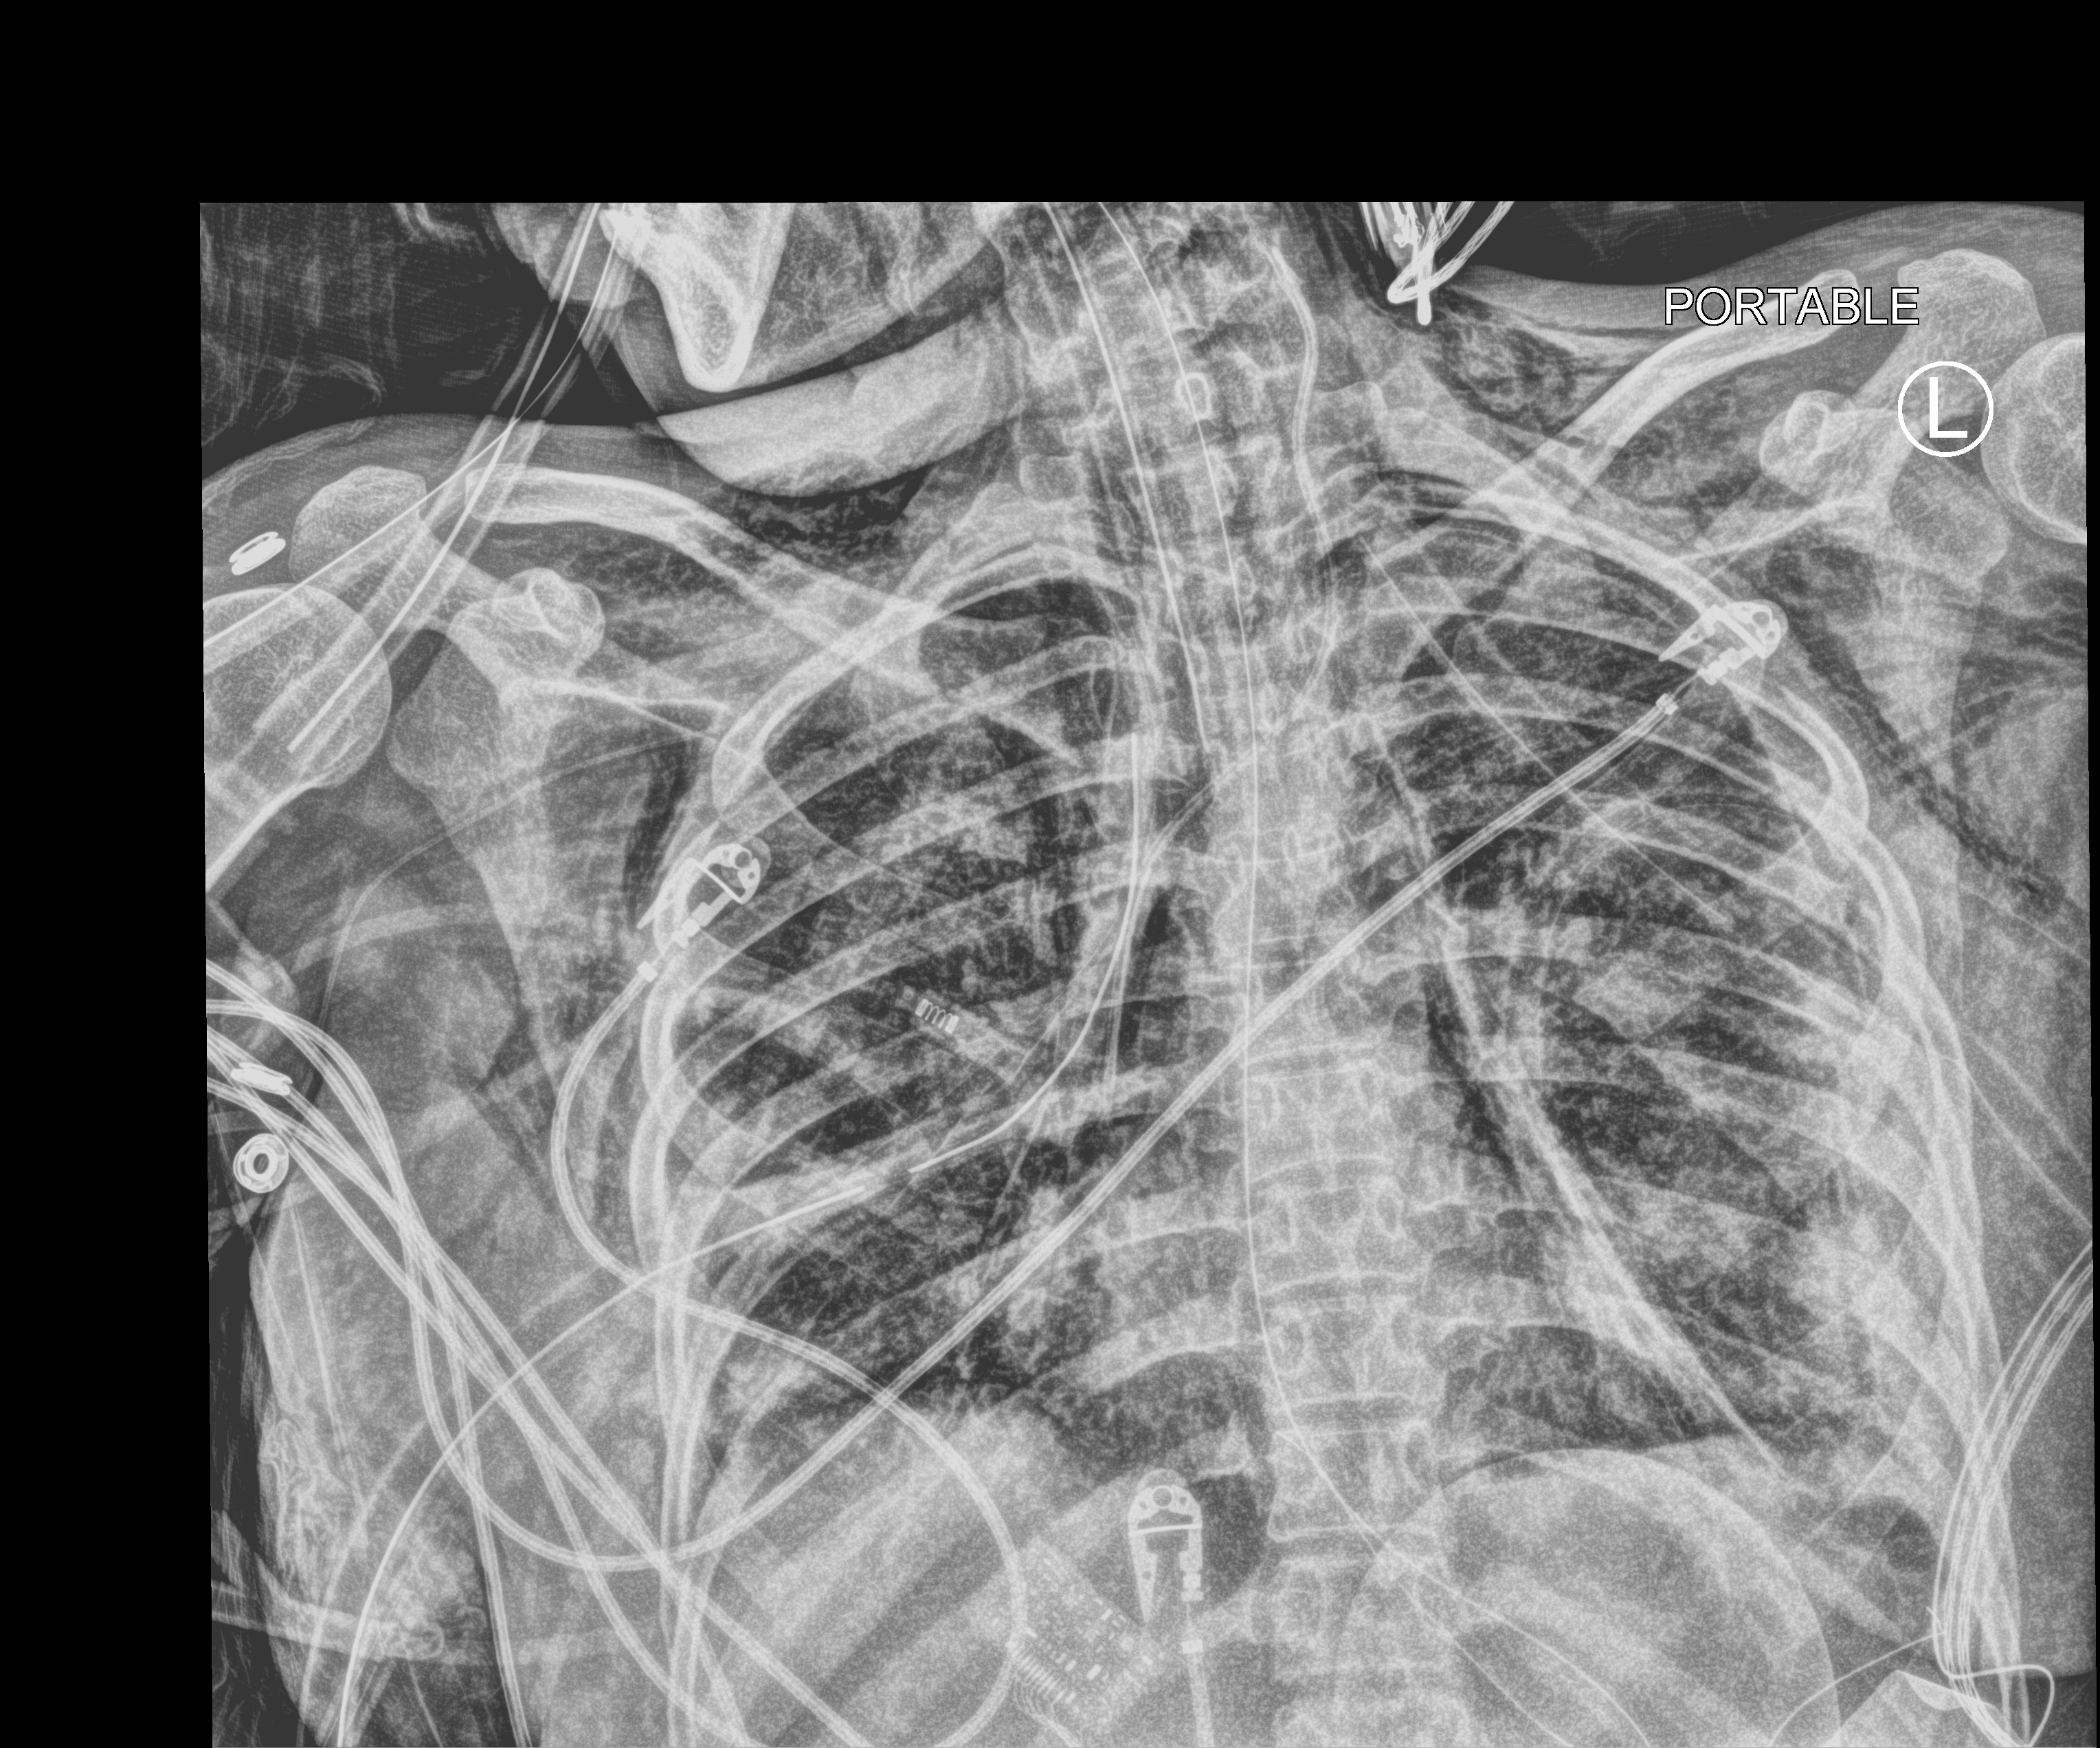
Portable chest radiograph; anteroposterior (AP) projection. Patient hospitalised with COVID-19, aged 18–59 years.
From the hospital-stay record, not from the radiograph (when in the stay this image was taken is not recorded):
- admitted to intensive care during this hospital stay: yes
- mechanically ventilated during this hospital stay: yes